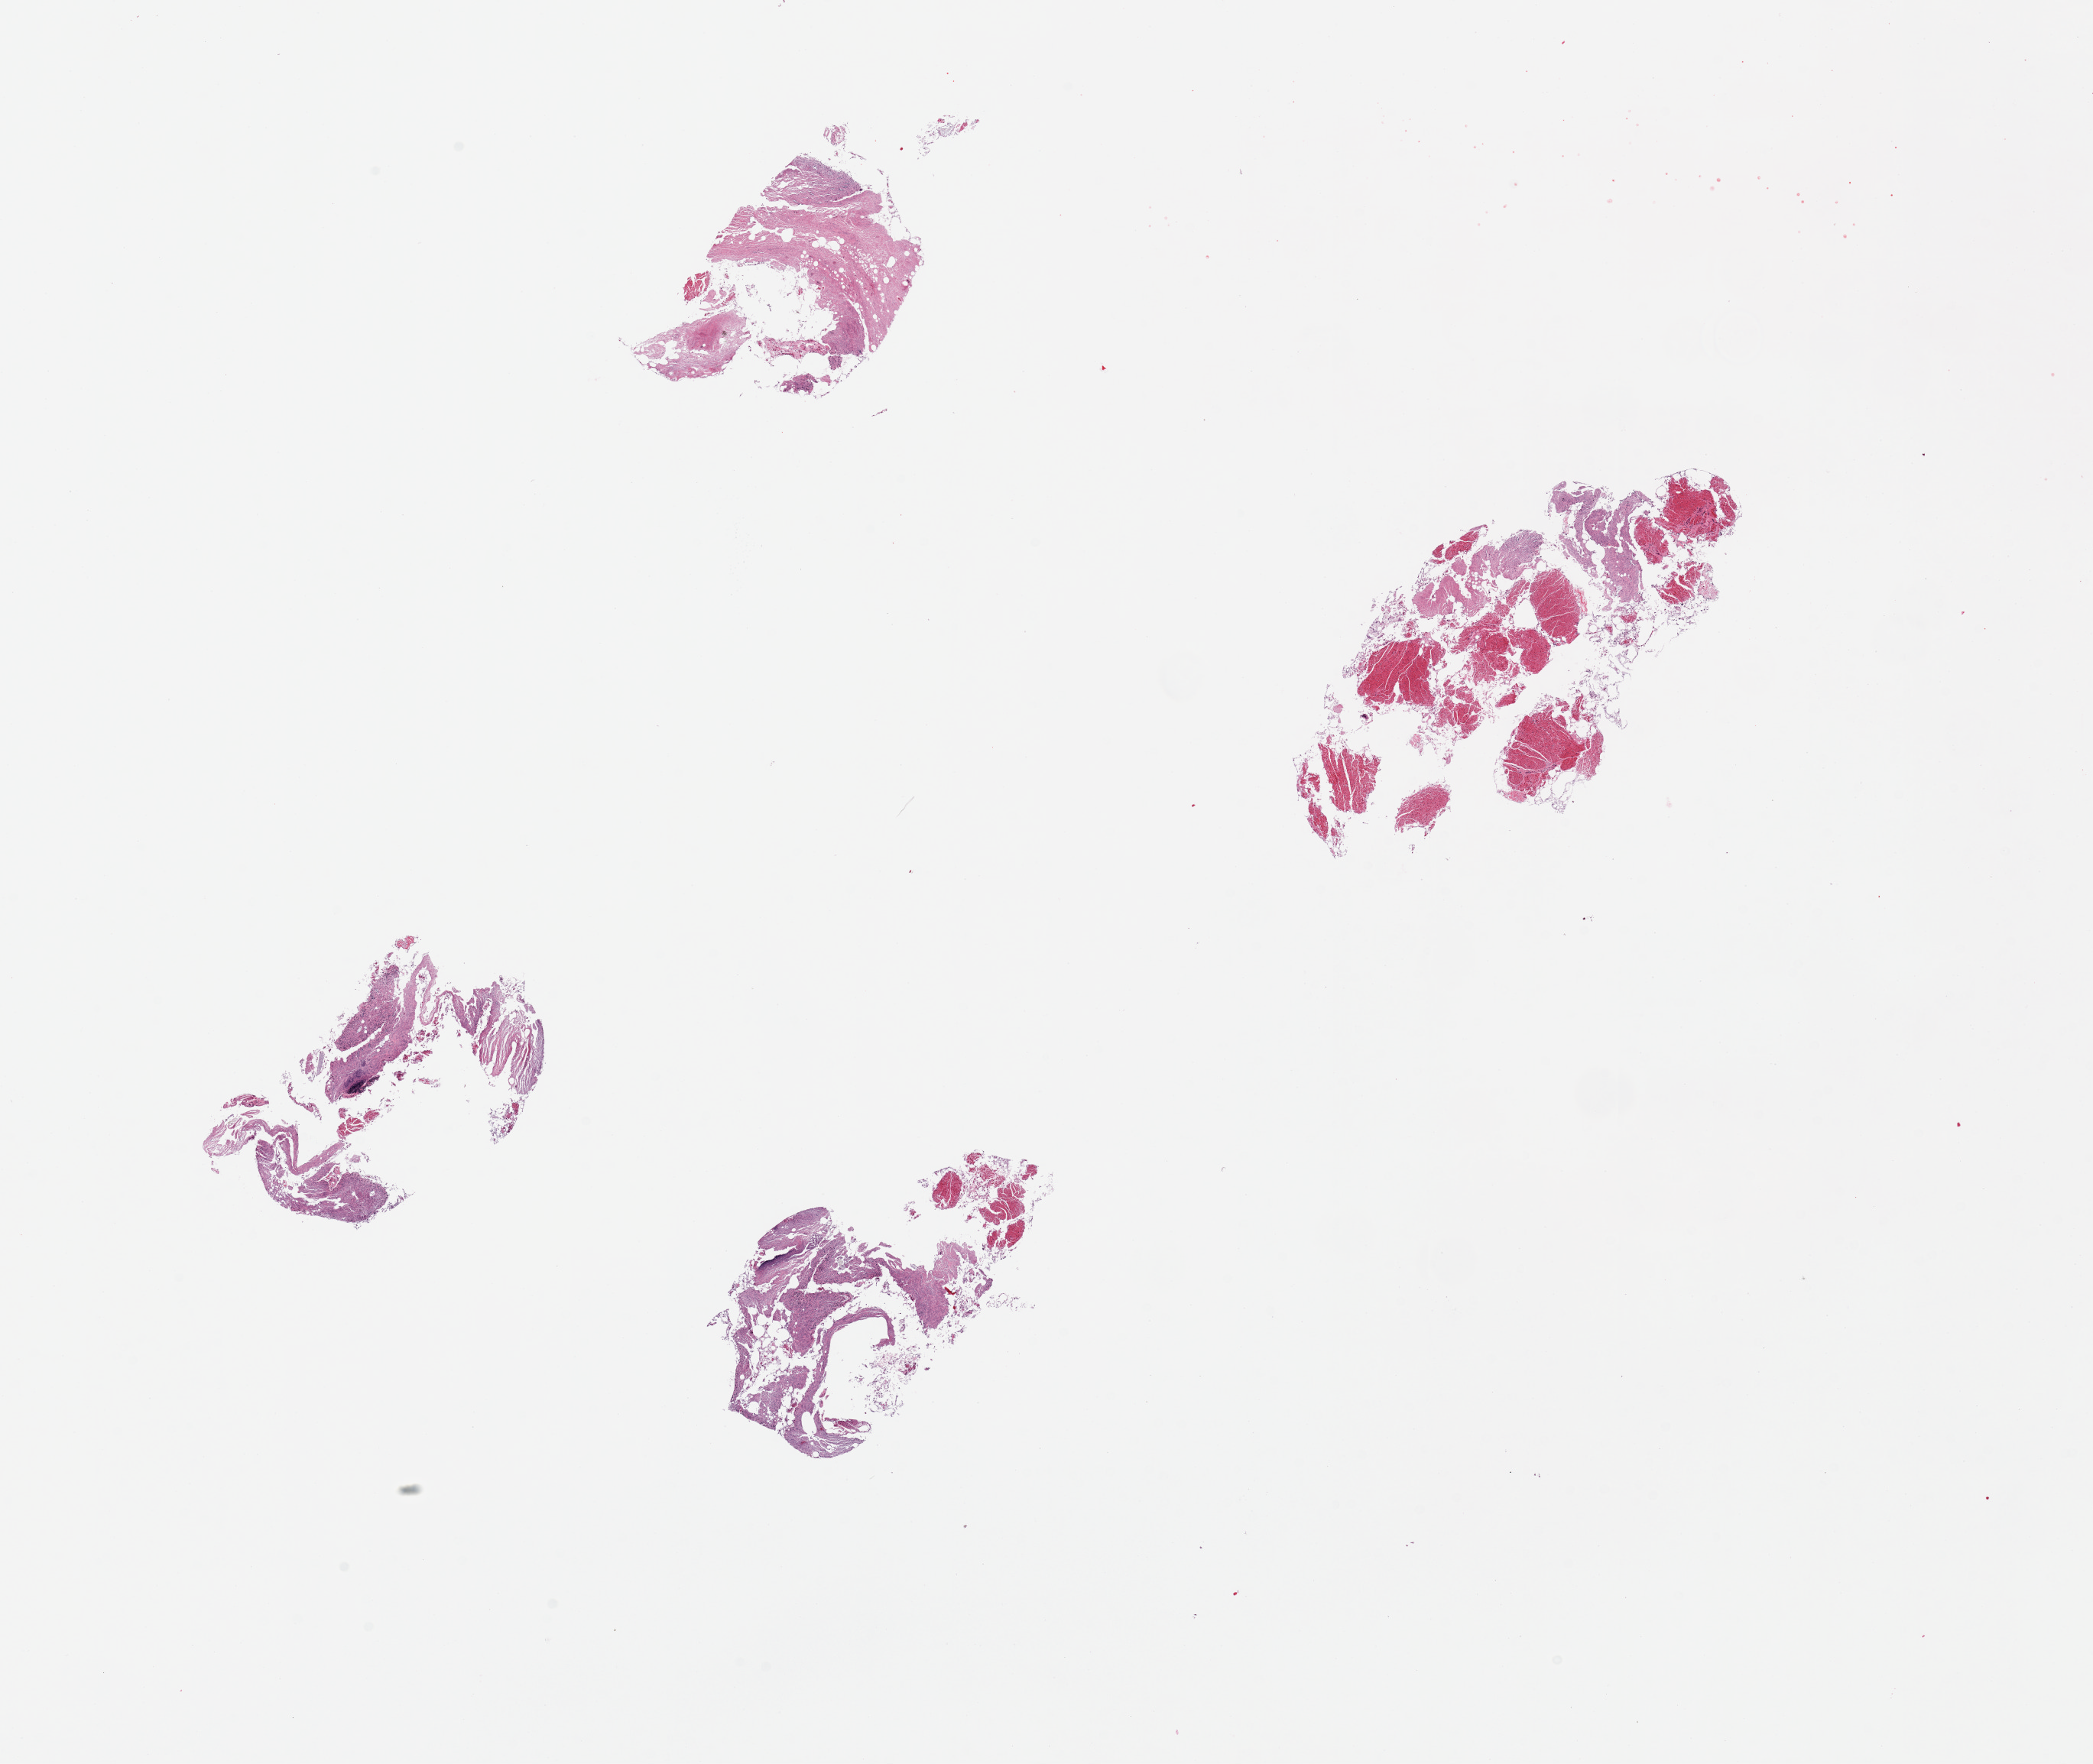
Whole-slide image, haematoxylin and eosin stain, low-resolution overview of the scanned area, about 21.7 x 18.3 mm. PAXgene-fixed paraffin-embedded (PFPE) section. Section of ileum (target tissue). Donor tissue sample.
Reviewer comment on this tissue sample: 4 pieces: no lymphoid tissue, no mucosa.